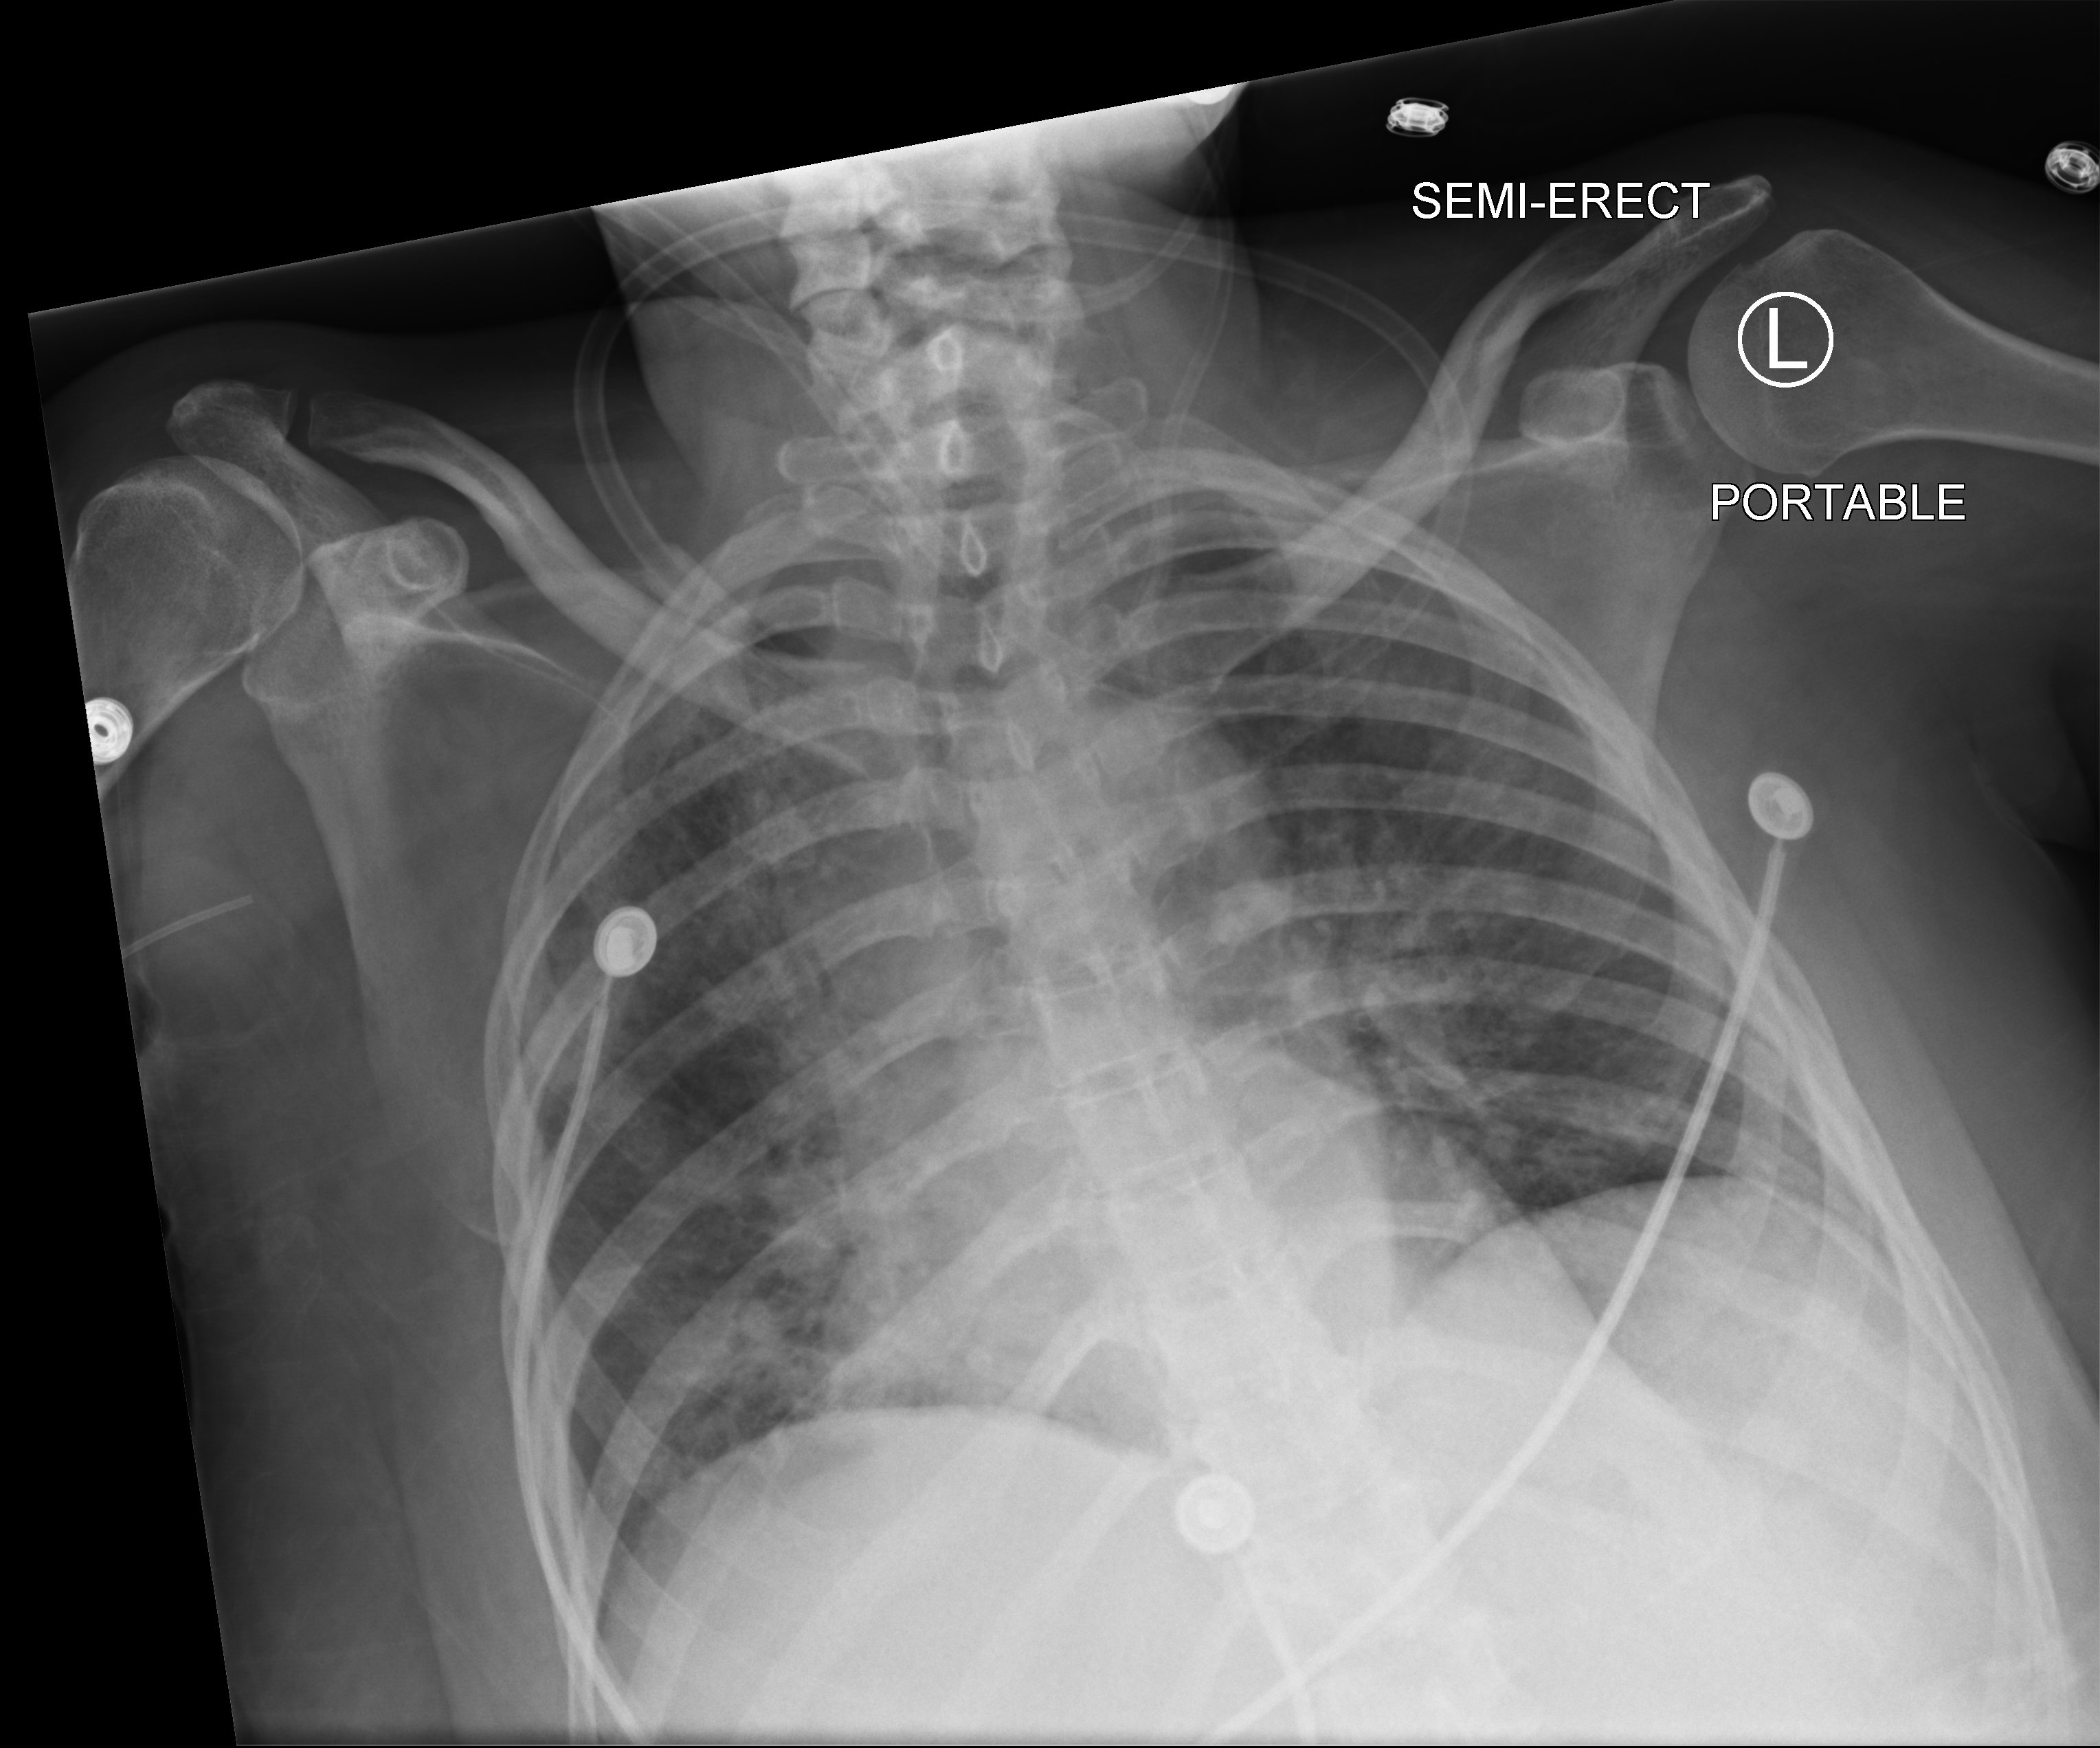
Bedside chest radiograph (computed radiography). Female patient hospitalised with COVID-19, age 18–59 years.
Hospital-stay facts (about this admission, not read from this image; timing relative to this image not recorded): admitted to intensive care during this hospital stay: no; mechanically ventilated during this hospital stay: no.